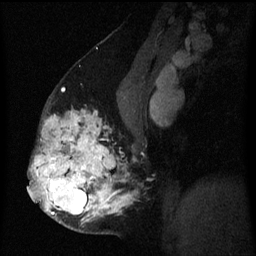
Breast MRI (dynamic contrast-enhanced), one sagittal slice; position 33 of 60 along the scan axis; dynamic contrast-enhanced series, image 2 of 3 at this slice position (ordered by acquisition); 1.5 T; TE 4.2 ms, TR 8 ms; 2 mm slice thickness; 256 × 256 image matrix. Patient: female, 50 years.
Annotated regions visible in this slice (semi-automatic segmentation, software-assisted and operator-edited):
- analysis volume of interest (the breast-tissue region the enhancement analysis was run in; not a lesion): box from (x=32, y=105) to (x=131, y=233) px
- tumour enhancement mask (voxels above the 70 % enhancement threshold inside the analysis volume of interest): (x=32, y=110)–(x=131, y=221)